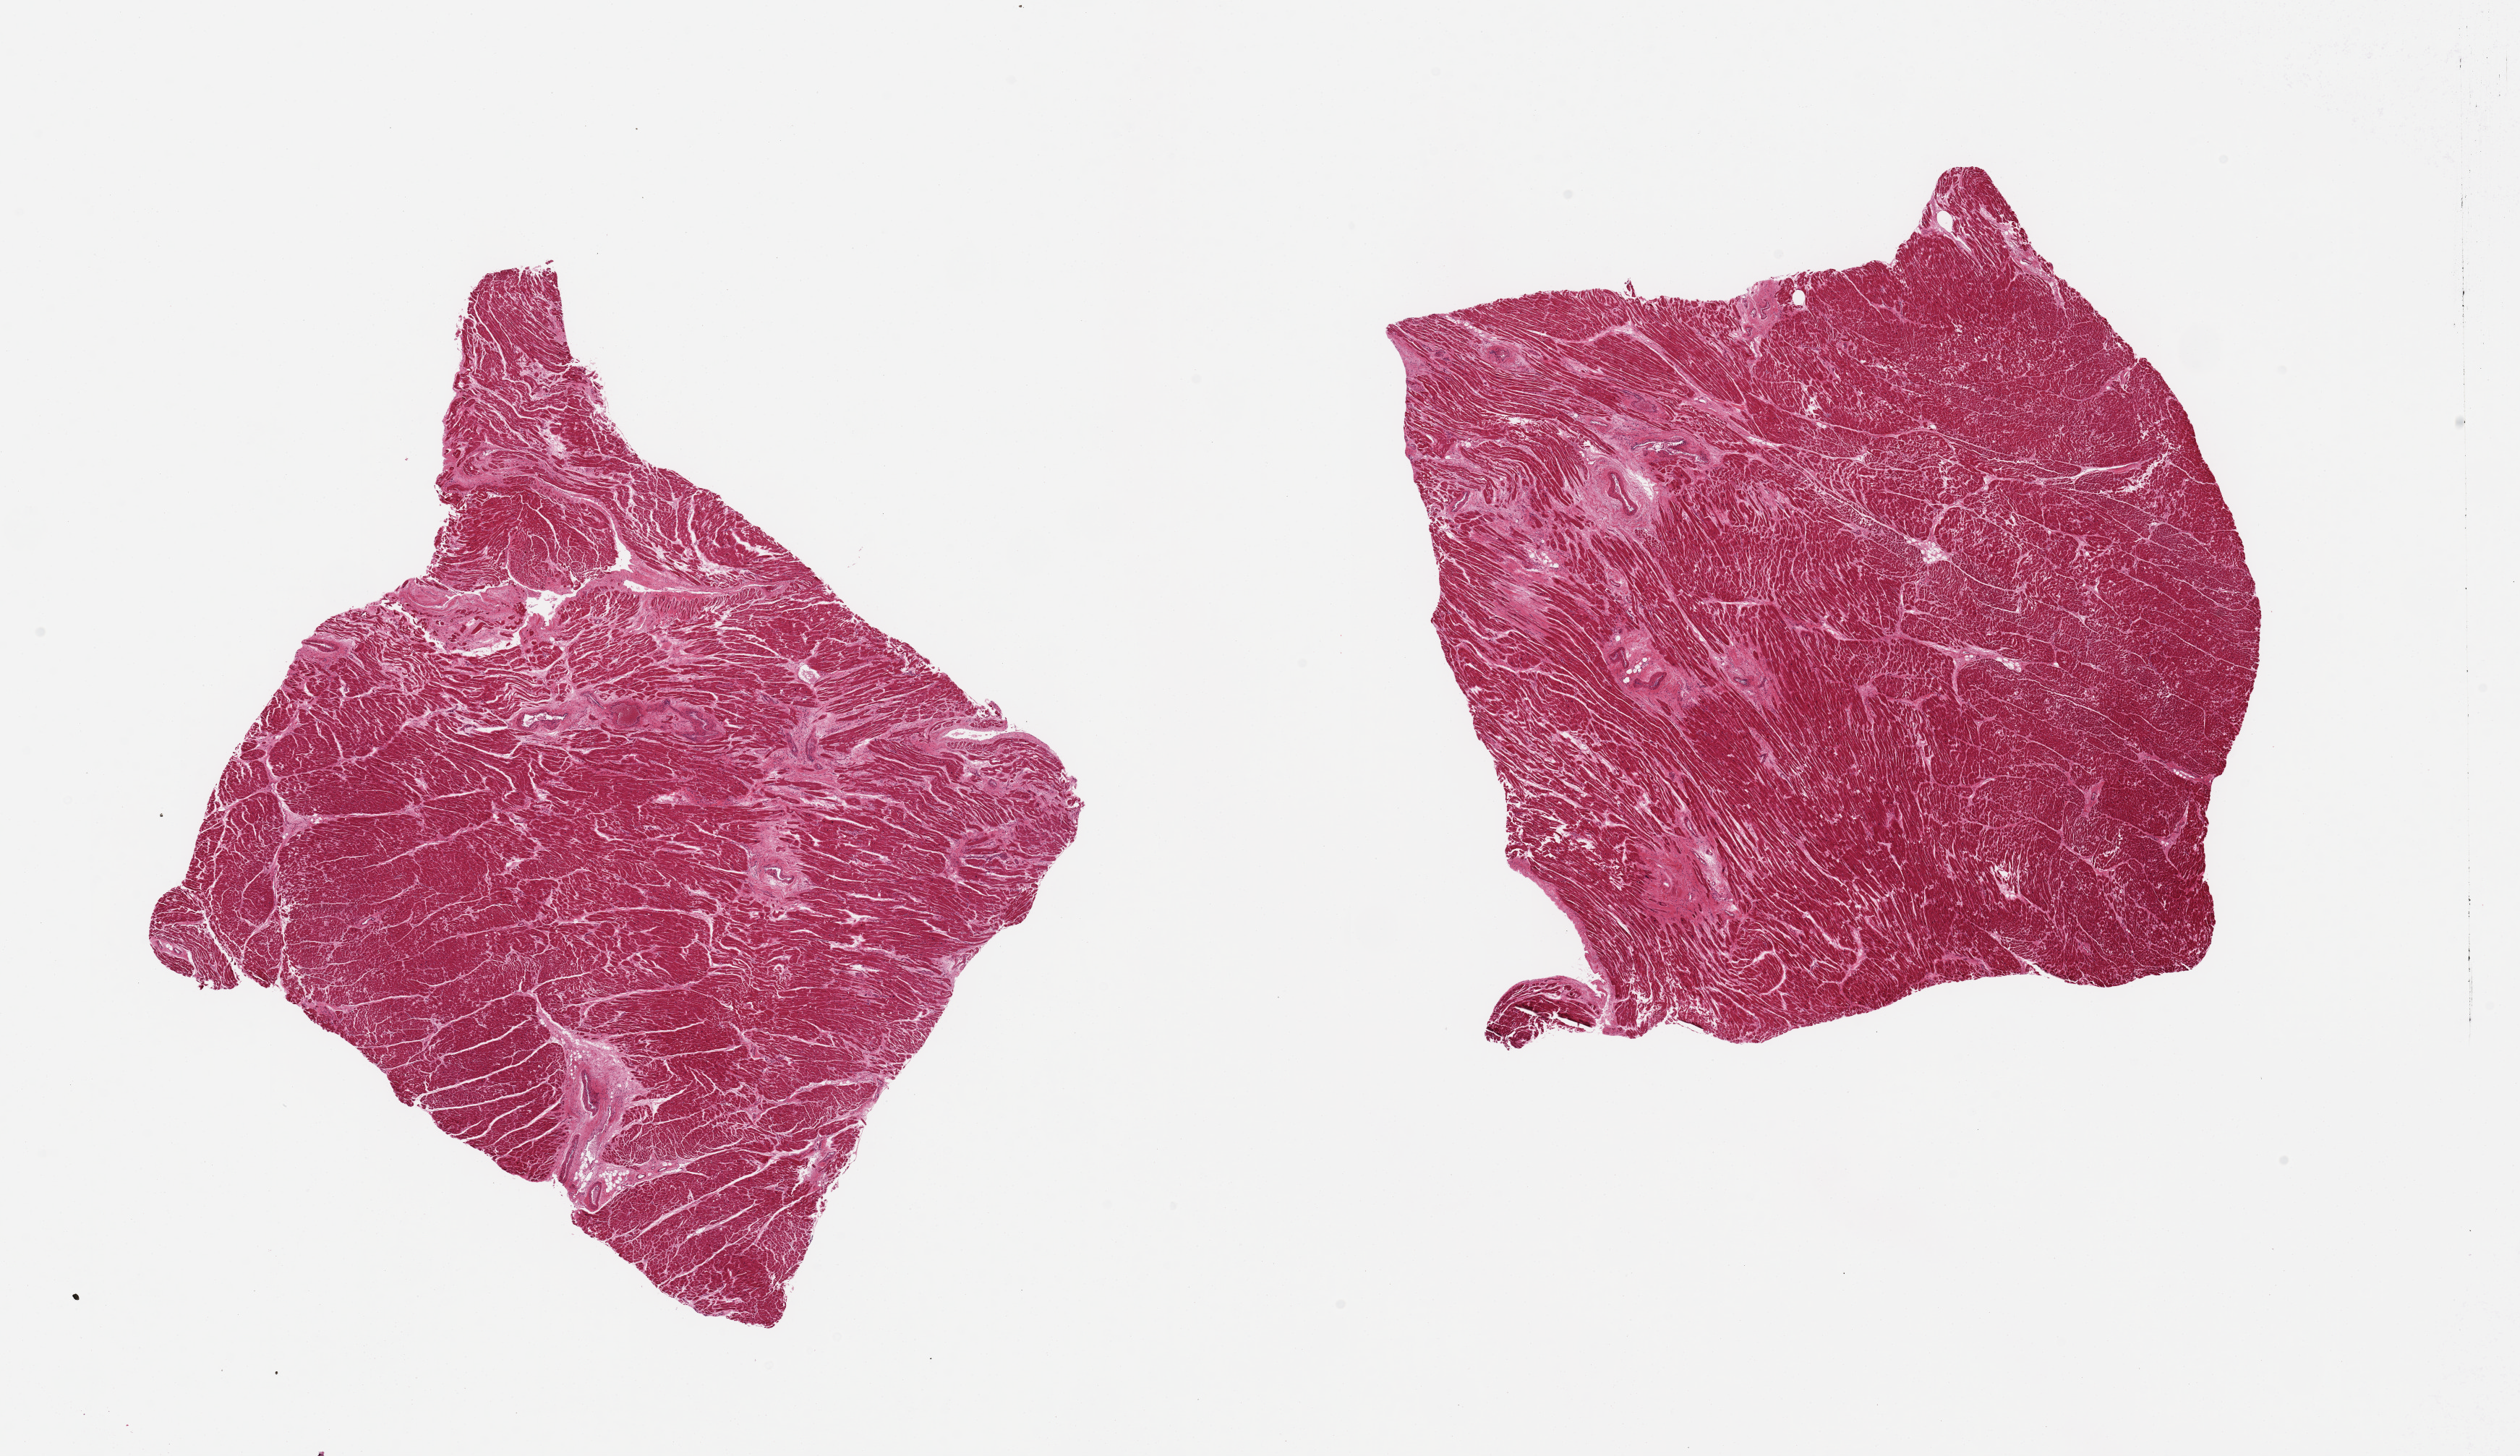
Haematoxylin and eosin whole-slide image, whole scanned area (about 27.6 x 15.9 mm) shown as a low-resolution overview. PAXgene-fixed, paraffin-embedded tissue. Sampled site (target tissue): heart. Donor tissue sample.
Reviewer comment on this tissue sample: 2 pieces; interstitial fibrosis with scarring.